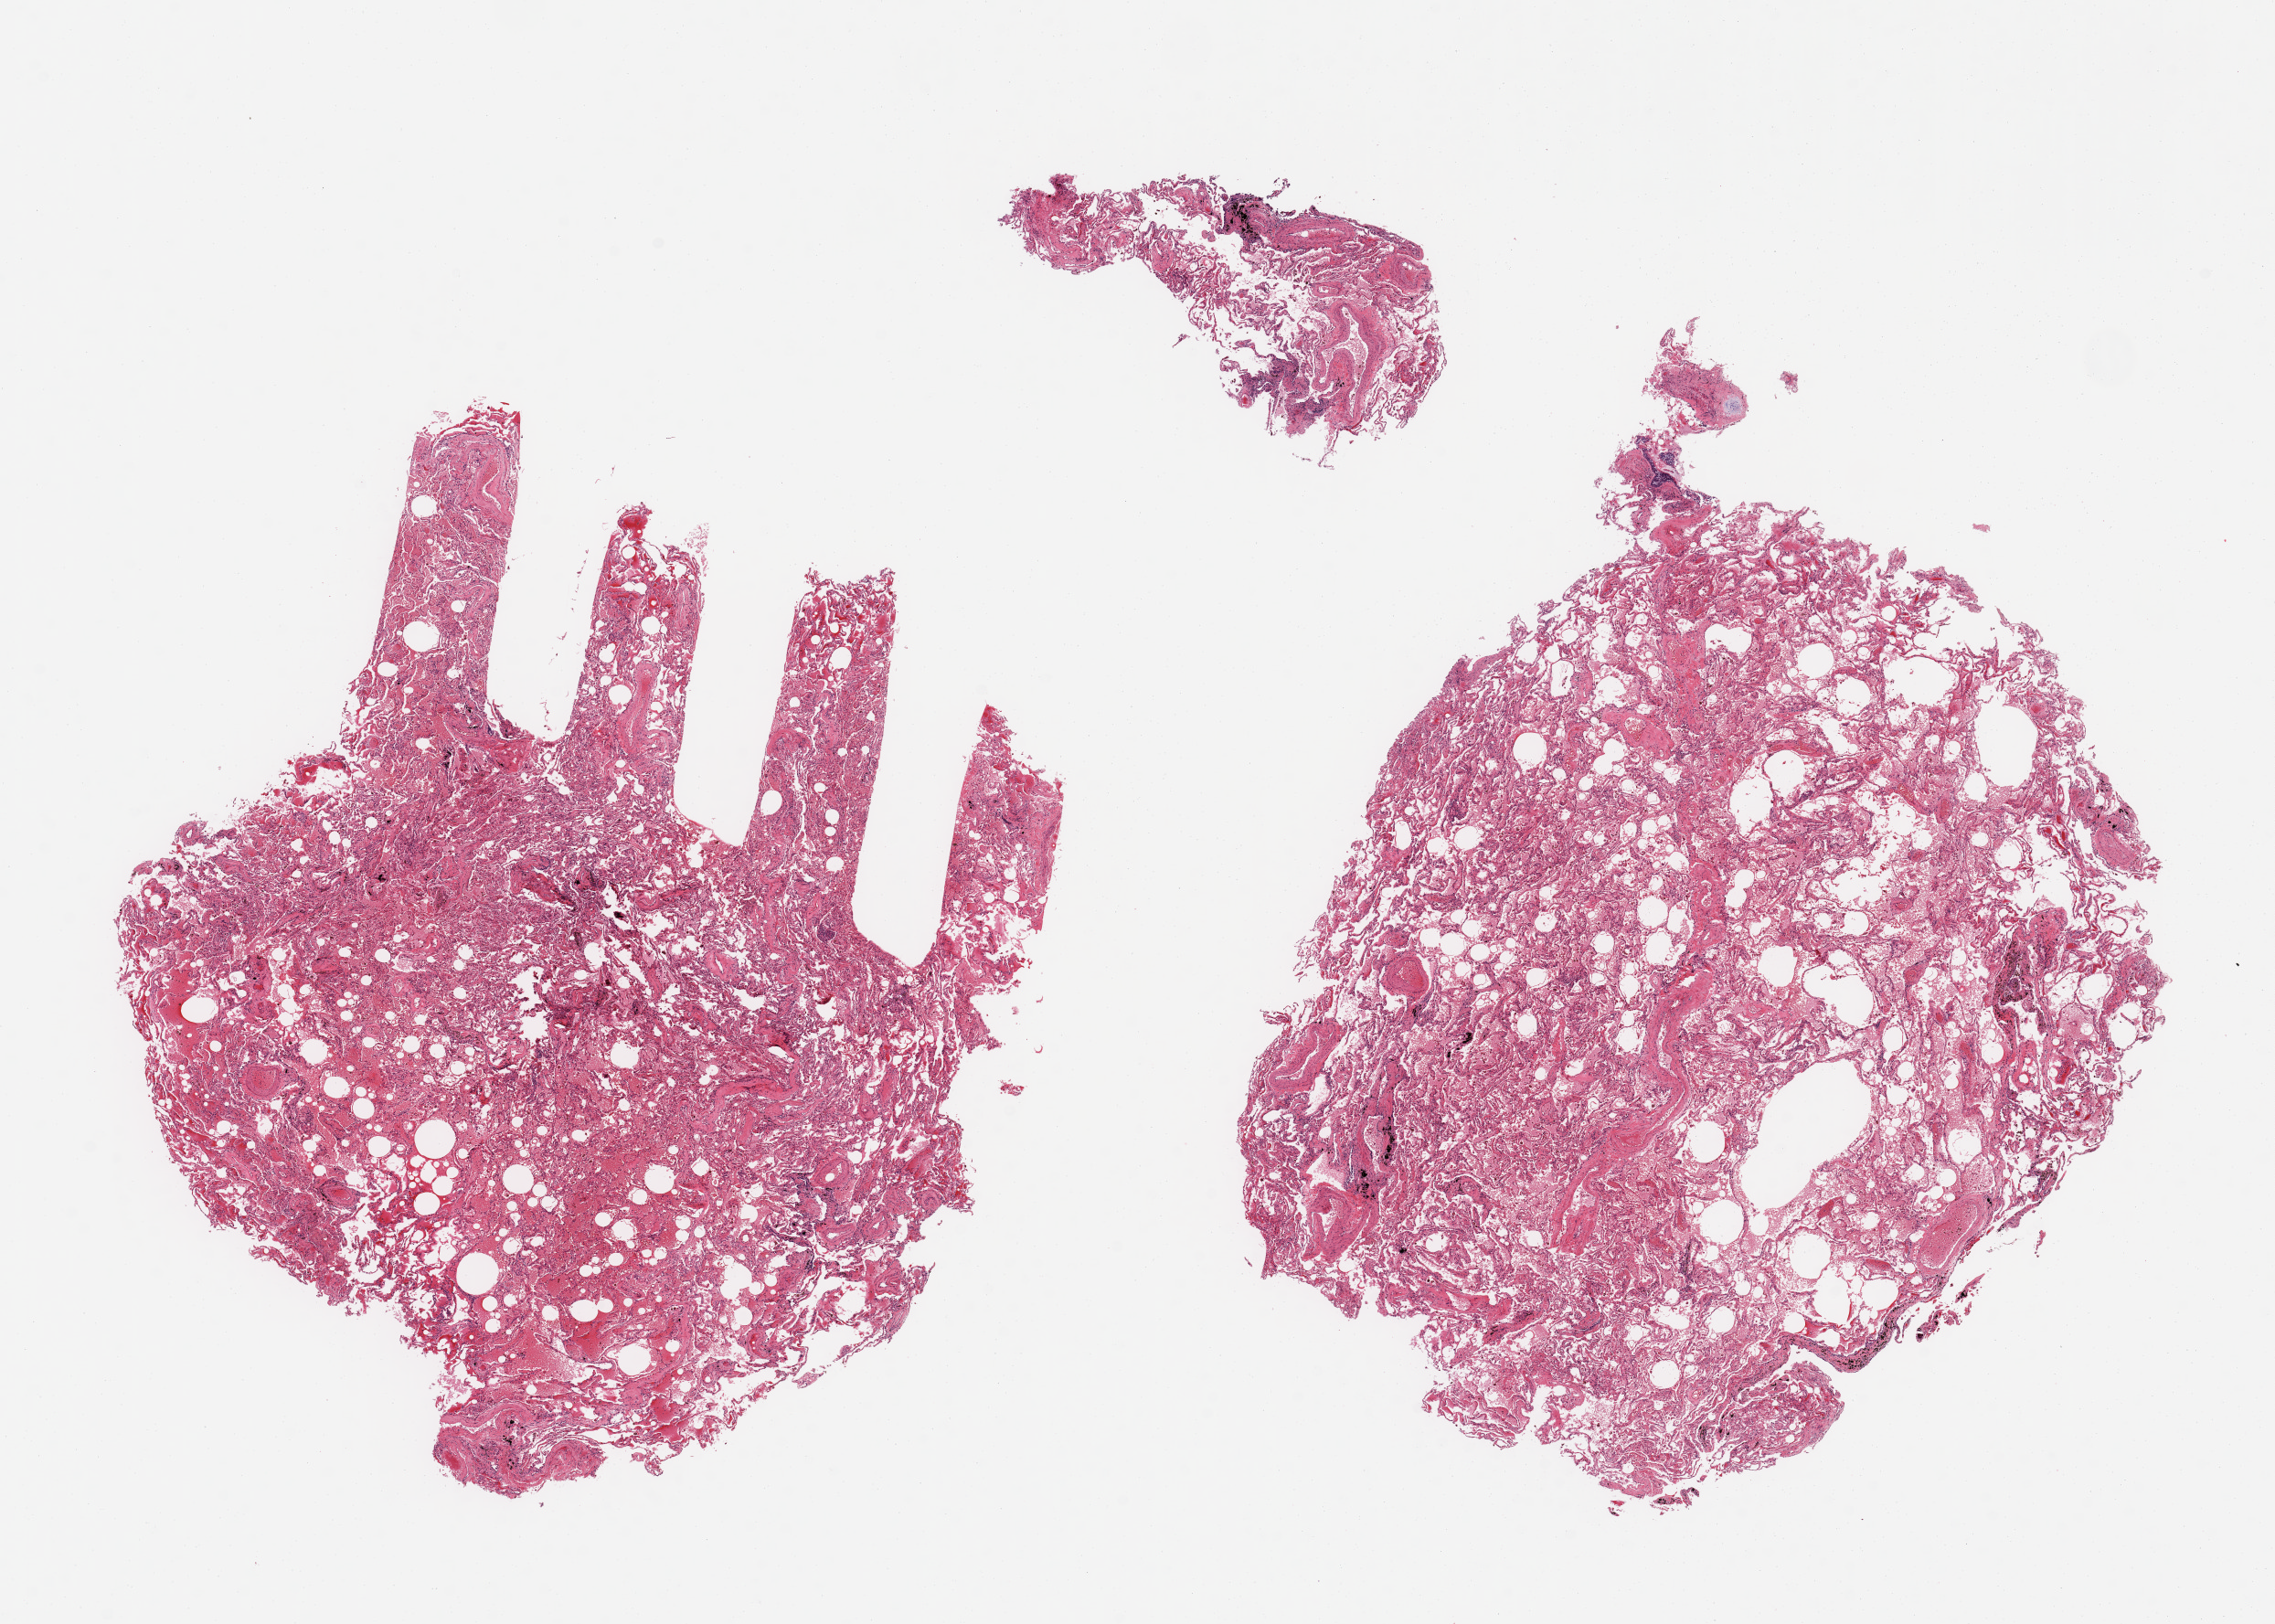
H&E whole-slide image, whole scanned area (about 19.7 x 14.1 mm, from a 20x scan) shown as a low-resolution overview, PAXgene-fixed, paraffin-embedded tissue, target tissue: lung, tissue donor sample. Male donor.
• pathologist's review note for this sample: 2 pieces, modearate congestion